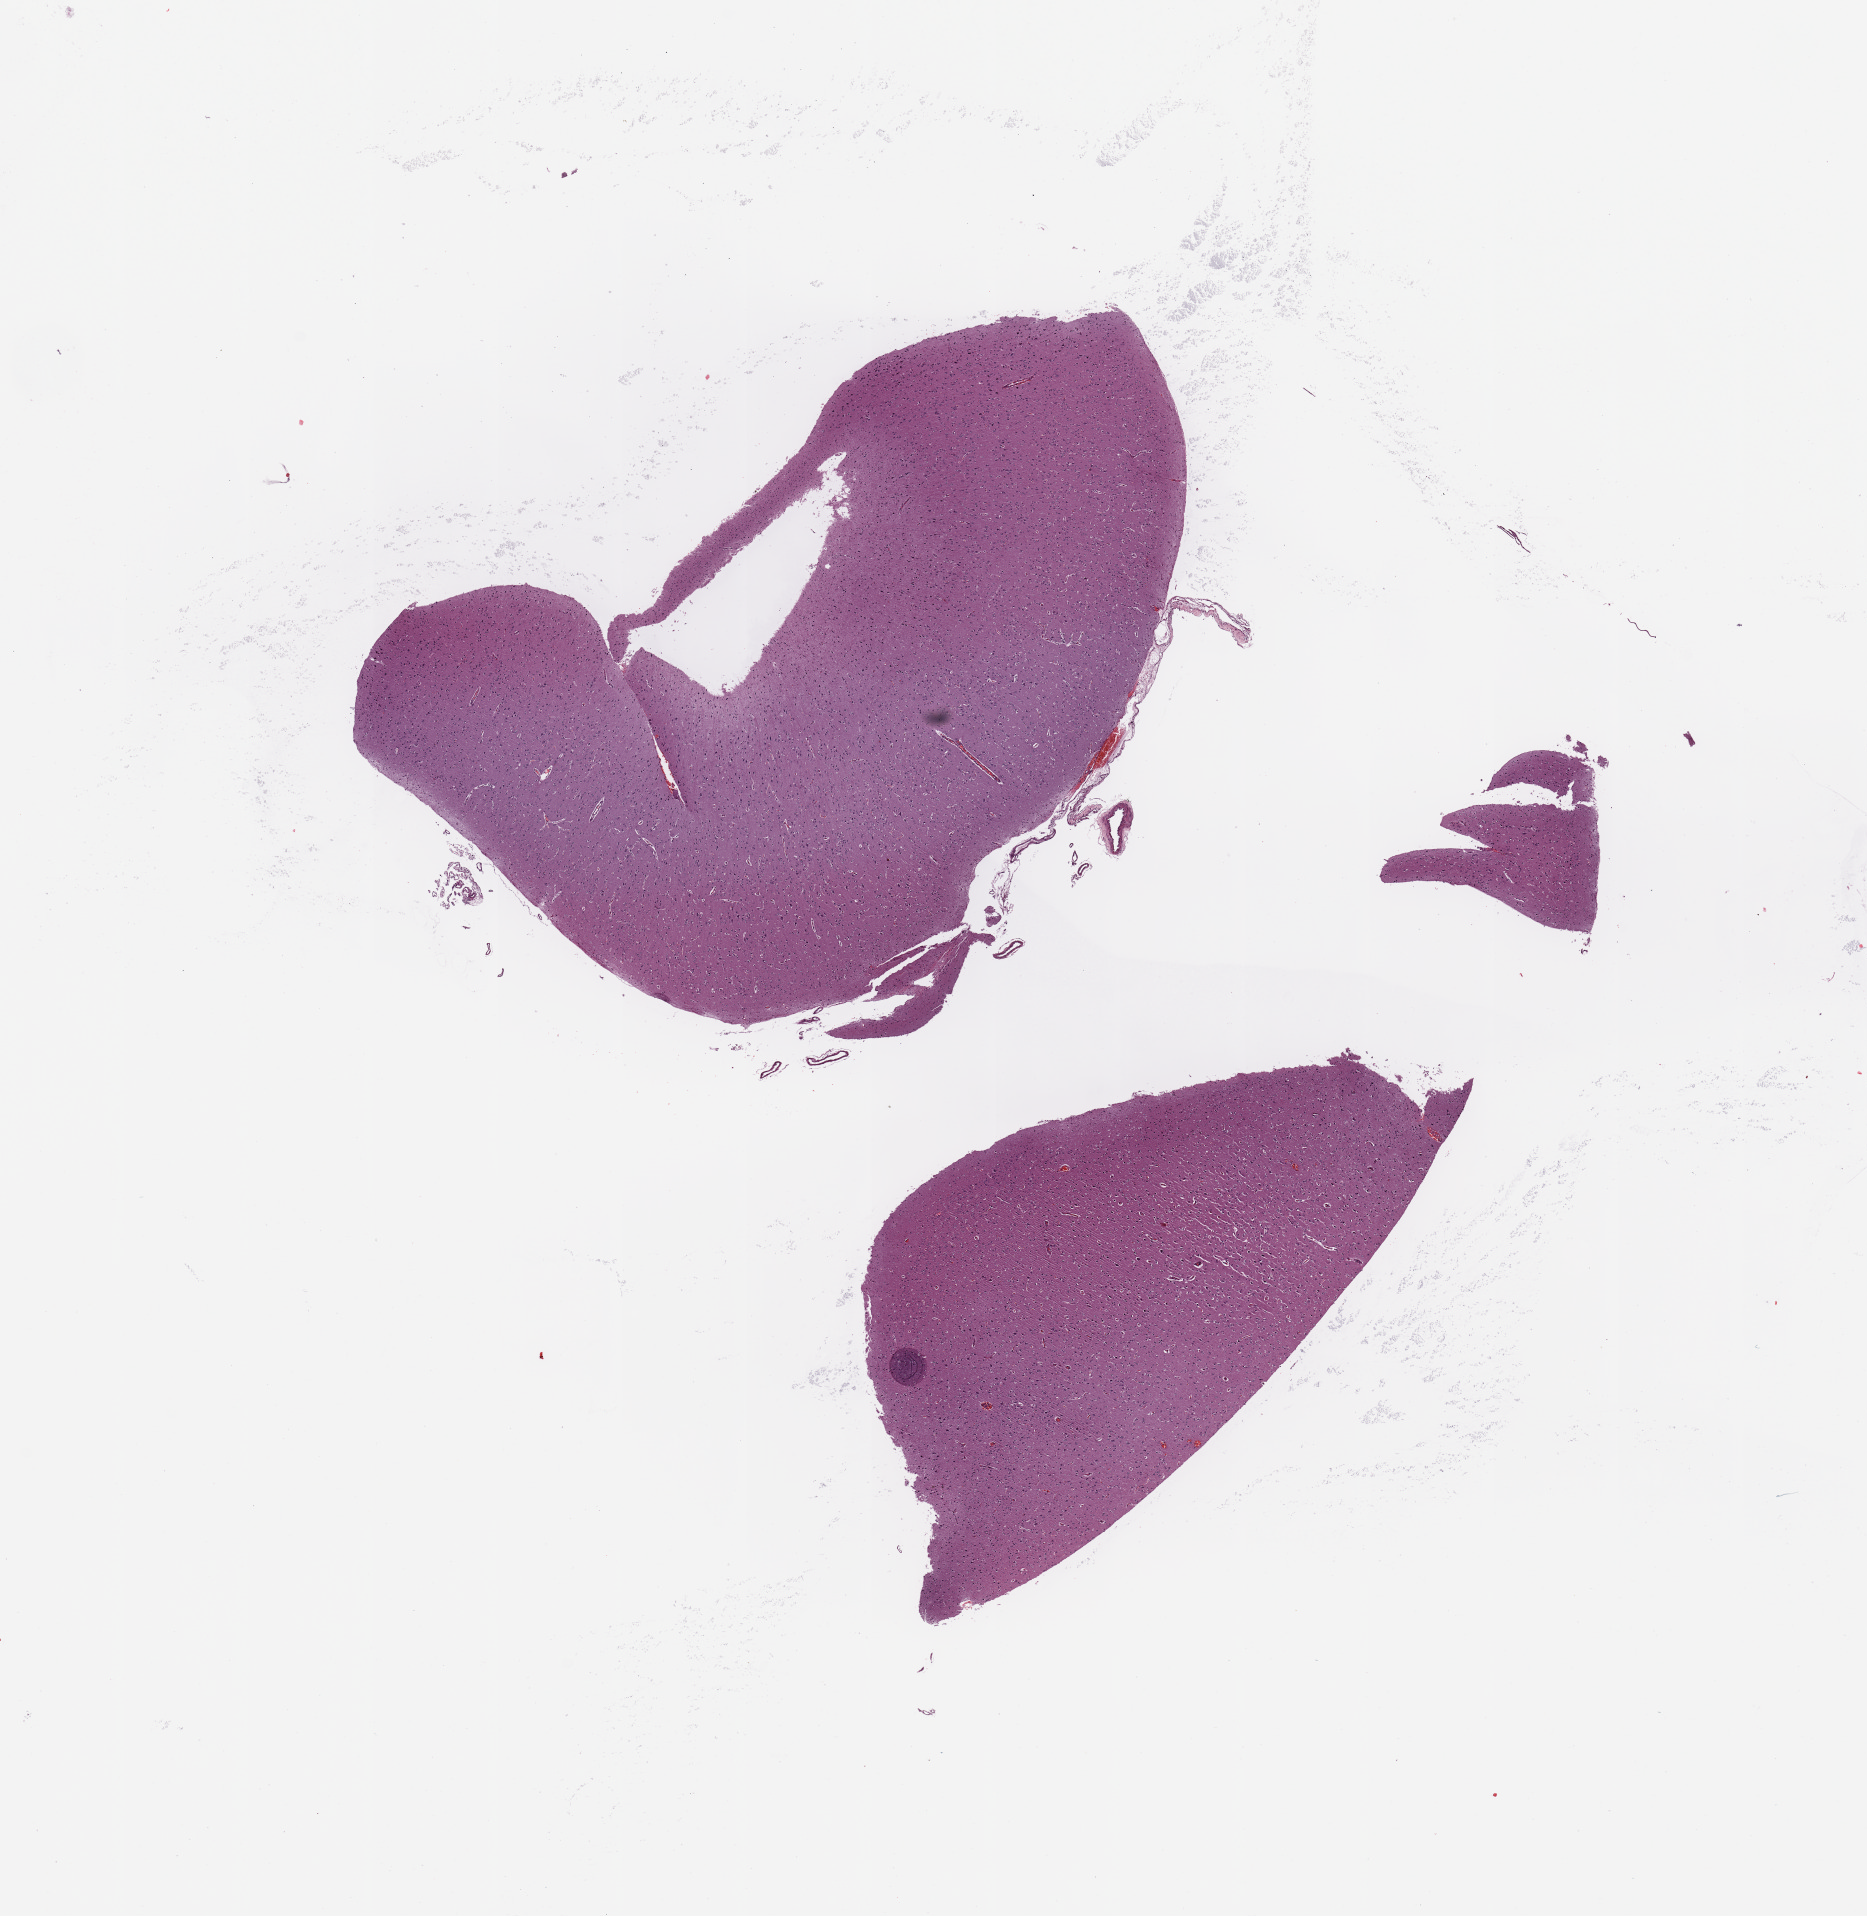
H&E whole-slide image, whole scanned area (about 14.8 x 15.2 mm) shown as a low-resolution overview, tumour tissue sample, brain. 53-year-old male patient.
* diagnosis: Glioblastoma
* primary tumour site (as recorded): frontal lobe